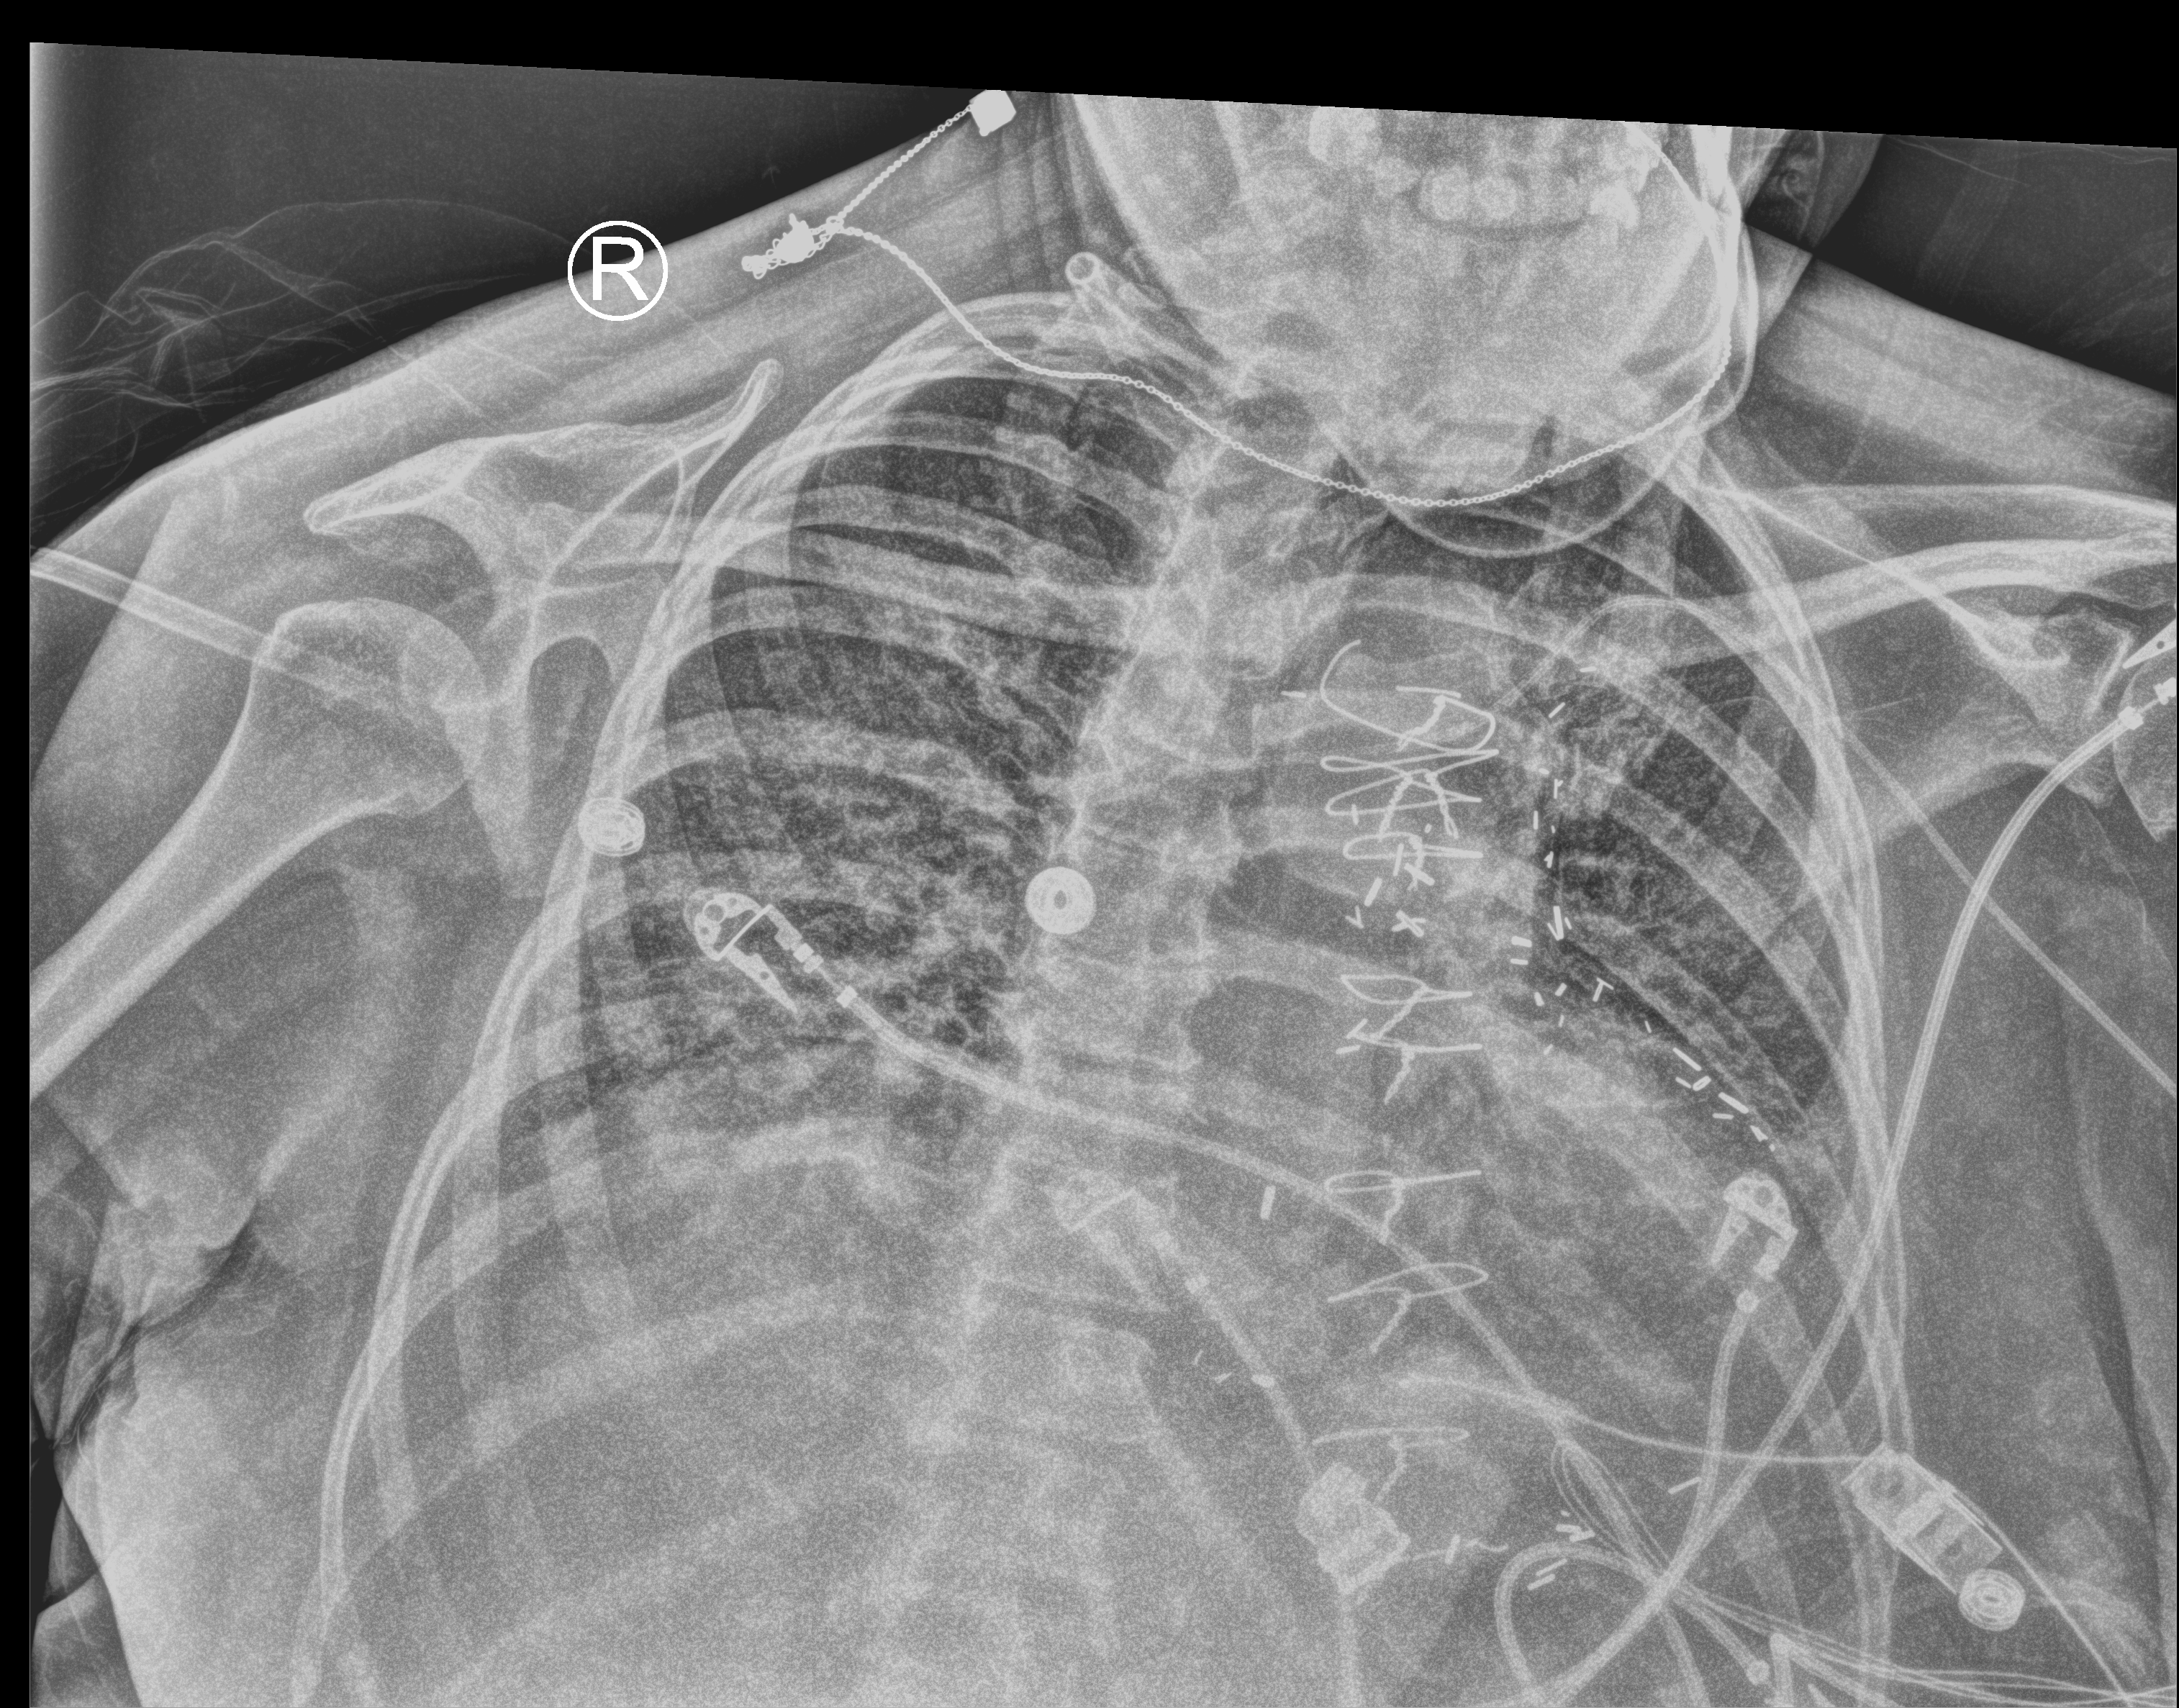
Bedside chest radiograph (computed radiography), anteroposterior (AP) projection. Female patient hospitalised with COVID-19, age 60–74 years.
Admission-level facts for this patient (not findings on this image; timing relative to this image not recorded): admitted to intensive care during this hospital stay: yes; mechanically ventilated during this hospital stay: yes.